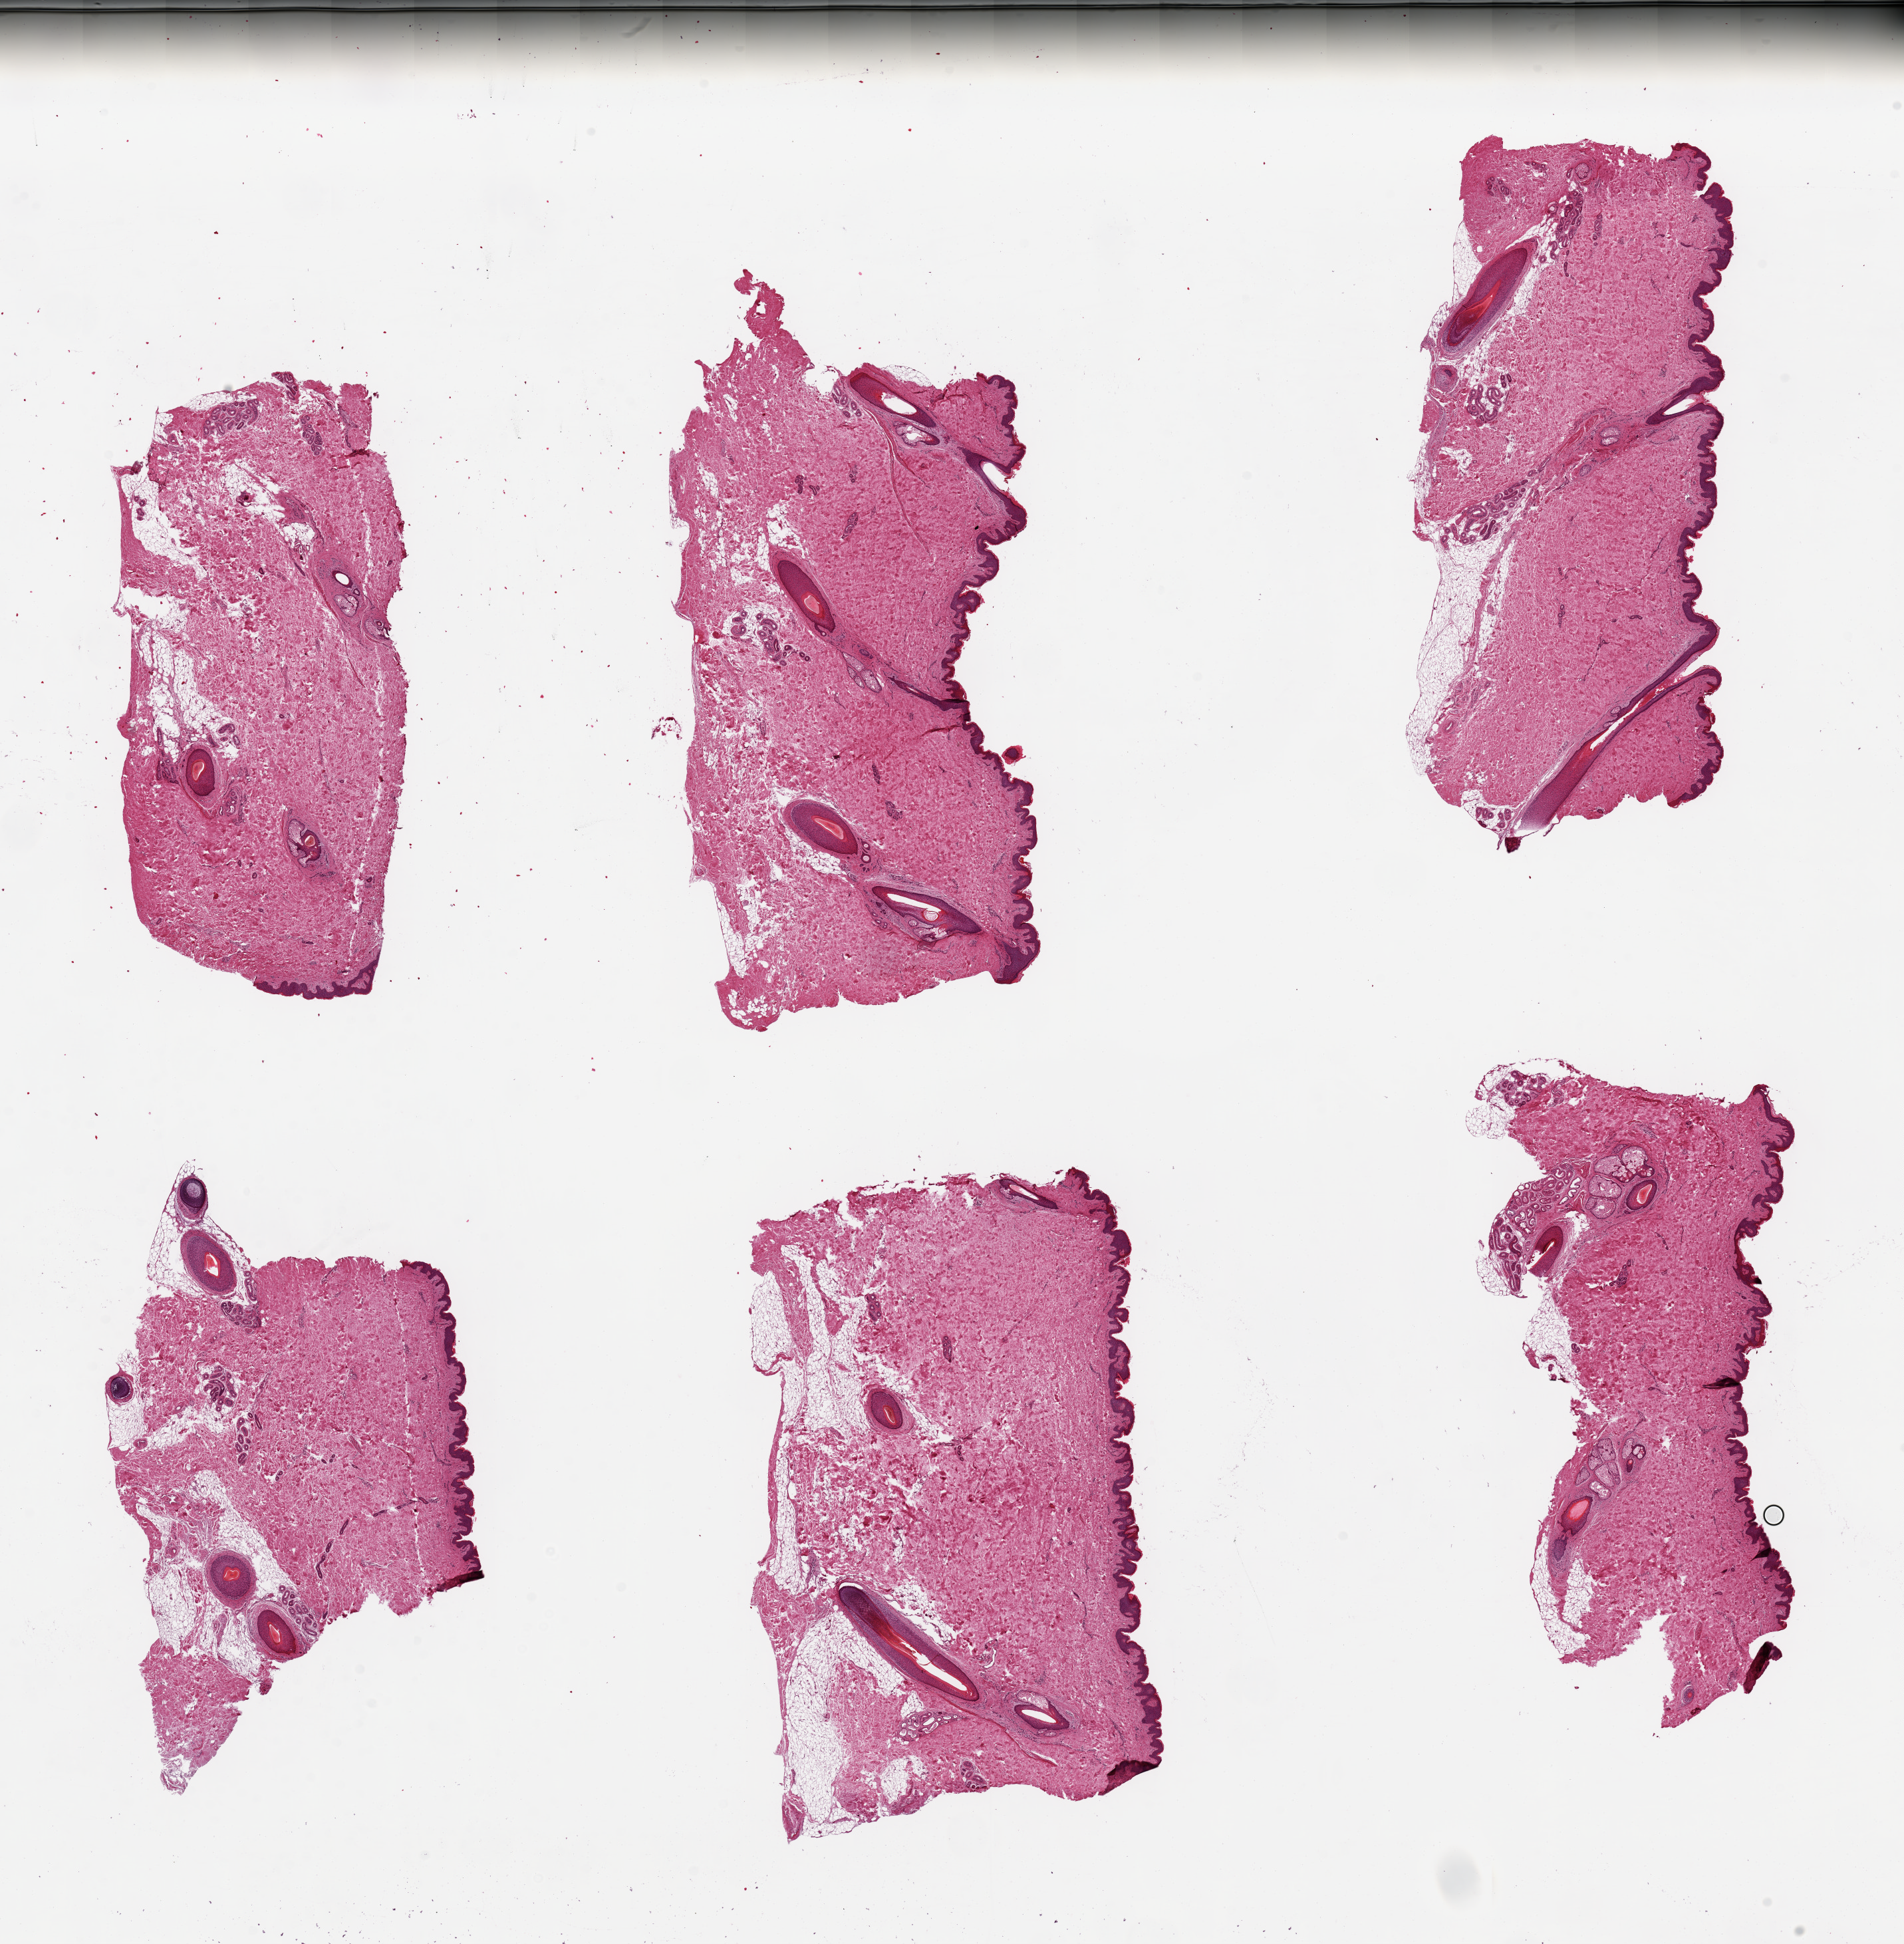
Hematoxylin and eosin (H&E) whole-slide image — whole scanned area (about 22.6 x 23.1 mm) shown as a low-resolution overview; PAXgene-fixed paraffin-embedded (PFPE) section; sampled site (target tissue): skin of suprapubic region; tissue donor sample. Male donor.
Pathologist's review note for this sample: 6 pieces, up to 8x5mm; squamous epithelium is ~1-2% thickness.